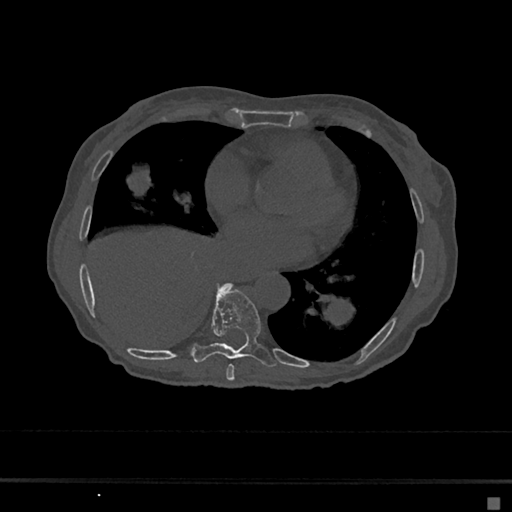
CT including the spine, one axial slice. Slice 327 of 797 in the series (ordered by position). Reconstruction kernel Br40s/3. Bone window (W 1800 / L 400 HU). 0.5 mm slice thickness. 512 × 512 image matrix. Female patient, age 68 years. Case-level facts recorded for this patient, not image findings: primary cancer: renal.
Structures marked on this image (semi-automatic segmentation, software-assisted and operator-edited):
- T7 vertebra: bounding box (x1, y1, x2, y2) in pixels: (226, 364, 235, 381)
- T8 vertebra: (191, 283, 276, 367)